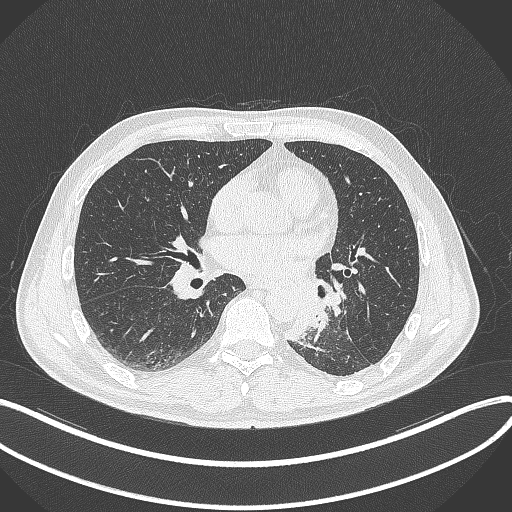
Chest CT, one axial slice. Reconstruction kernel B70f. Lung window (W 1500 / L -600 HU). 1 mm slice thickness. 512 × 512 image matrix, field of view 400 × 400 mm. Patient: male, 59 years. Case-level facts recorded for this patient, not image findings: clinical TNM (as recorded): T2a N2 M0.
Outlined on this slice (rectangle marked by the reading radiologist):
- lung tumour (recorded histology: squamous cell carcinoma): bounding box <285,288,331,347> (left, top, right, bottom; pixels)